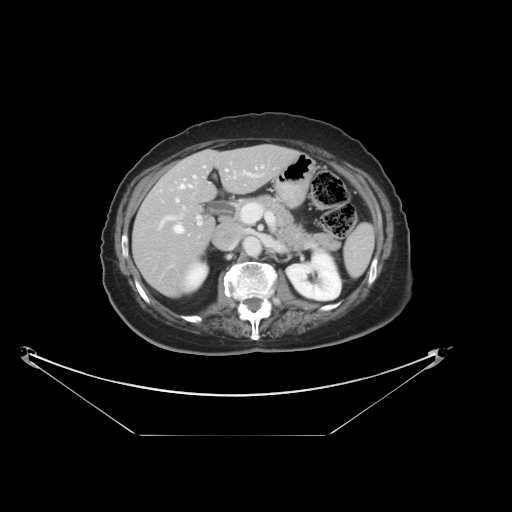
Contrast-enhanced abdominal CT, one axial slice; 120 kVp; intravenous contrast given; soft-tissue window (W 400 / L 40 HU); 5 mm slice thickness; 512 × 512 image matrix, field of view 500 × 500 mm. Female patient, age 70 years. Case-level facts recorded for this patient, not image findings: diagnosis: colorectal cancer liver metastases, imaged before liver resection; multiple liver metastases: no; largest metastasis: 2.5 cm; disease in both lobes: no.
Outlined on this slice (outlined manually by an expert reader):
- hepatic veins: bounding box [x1, y1, x2, y2] px = [174, 166, 263, 233]
- liver: [134, 145, 297, 297]
- planned liver remnant (the part of the liver to remain after resection): [134, 145, 297, 297]
- portal vein (with intrahepatic branches): [161, 171, 258, 226]